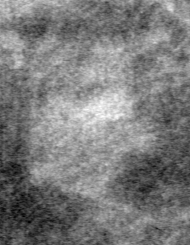
Region of interest cut from a scanned film mammogram (one marked finding); left breast; MLO view.
Marked abnormality: mass, shape lobulated, margins microlobulated; BI-RADS assessment category 4; subtlety rating 3 on a 1 (subtle) to 5 (obvious) scale; pathology result (as recorded, not read from the image): benign.